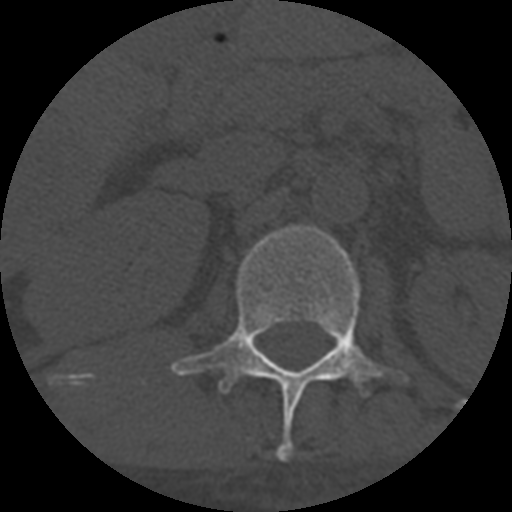
CT including the spine, one axial slice. Position 287 of 708 along the scan axis. Reconstruction kernel STANDARD. 120 kVp. One of 3 acquisitions stored at this slice position. Bone window (W 1800 / L 400 HU). 512 × 512 image matrix, field of view 160 × 160 mm. Patient age 55 years. From the clinical record (not read from this slice): primary cancer: colon; vertebrae with lytic lesions (as recorded): T12, L1, L5.
Annotated regions visible in this slice (semi-automatically segmented with operator editing):
- L1 vertebra: bounding box [x1, y1, x2, y2] px = [171, 226, 408, 461]